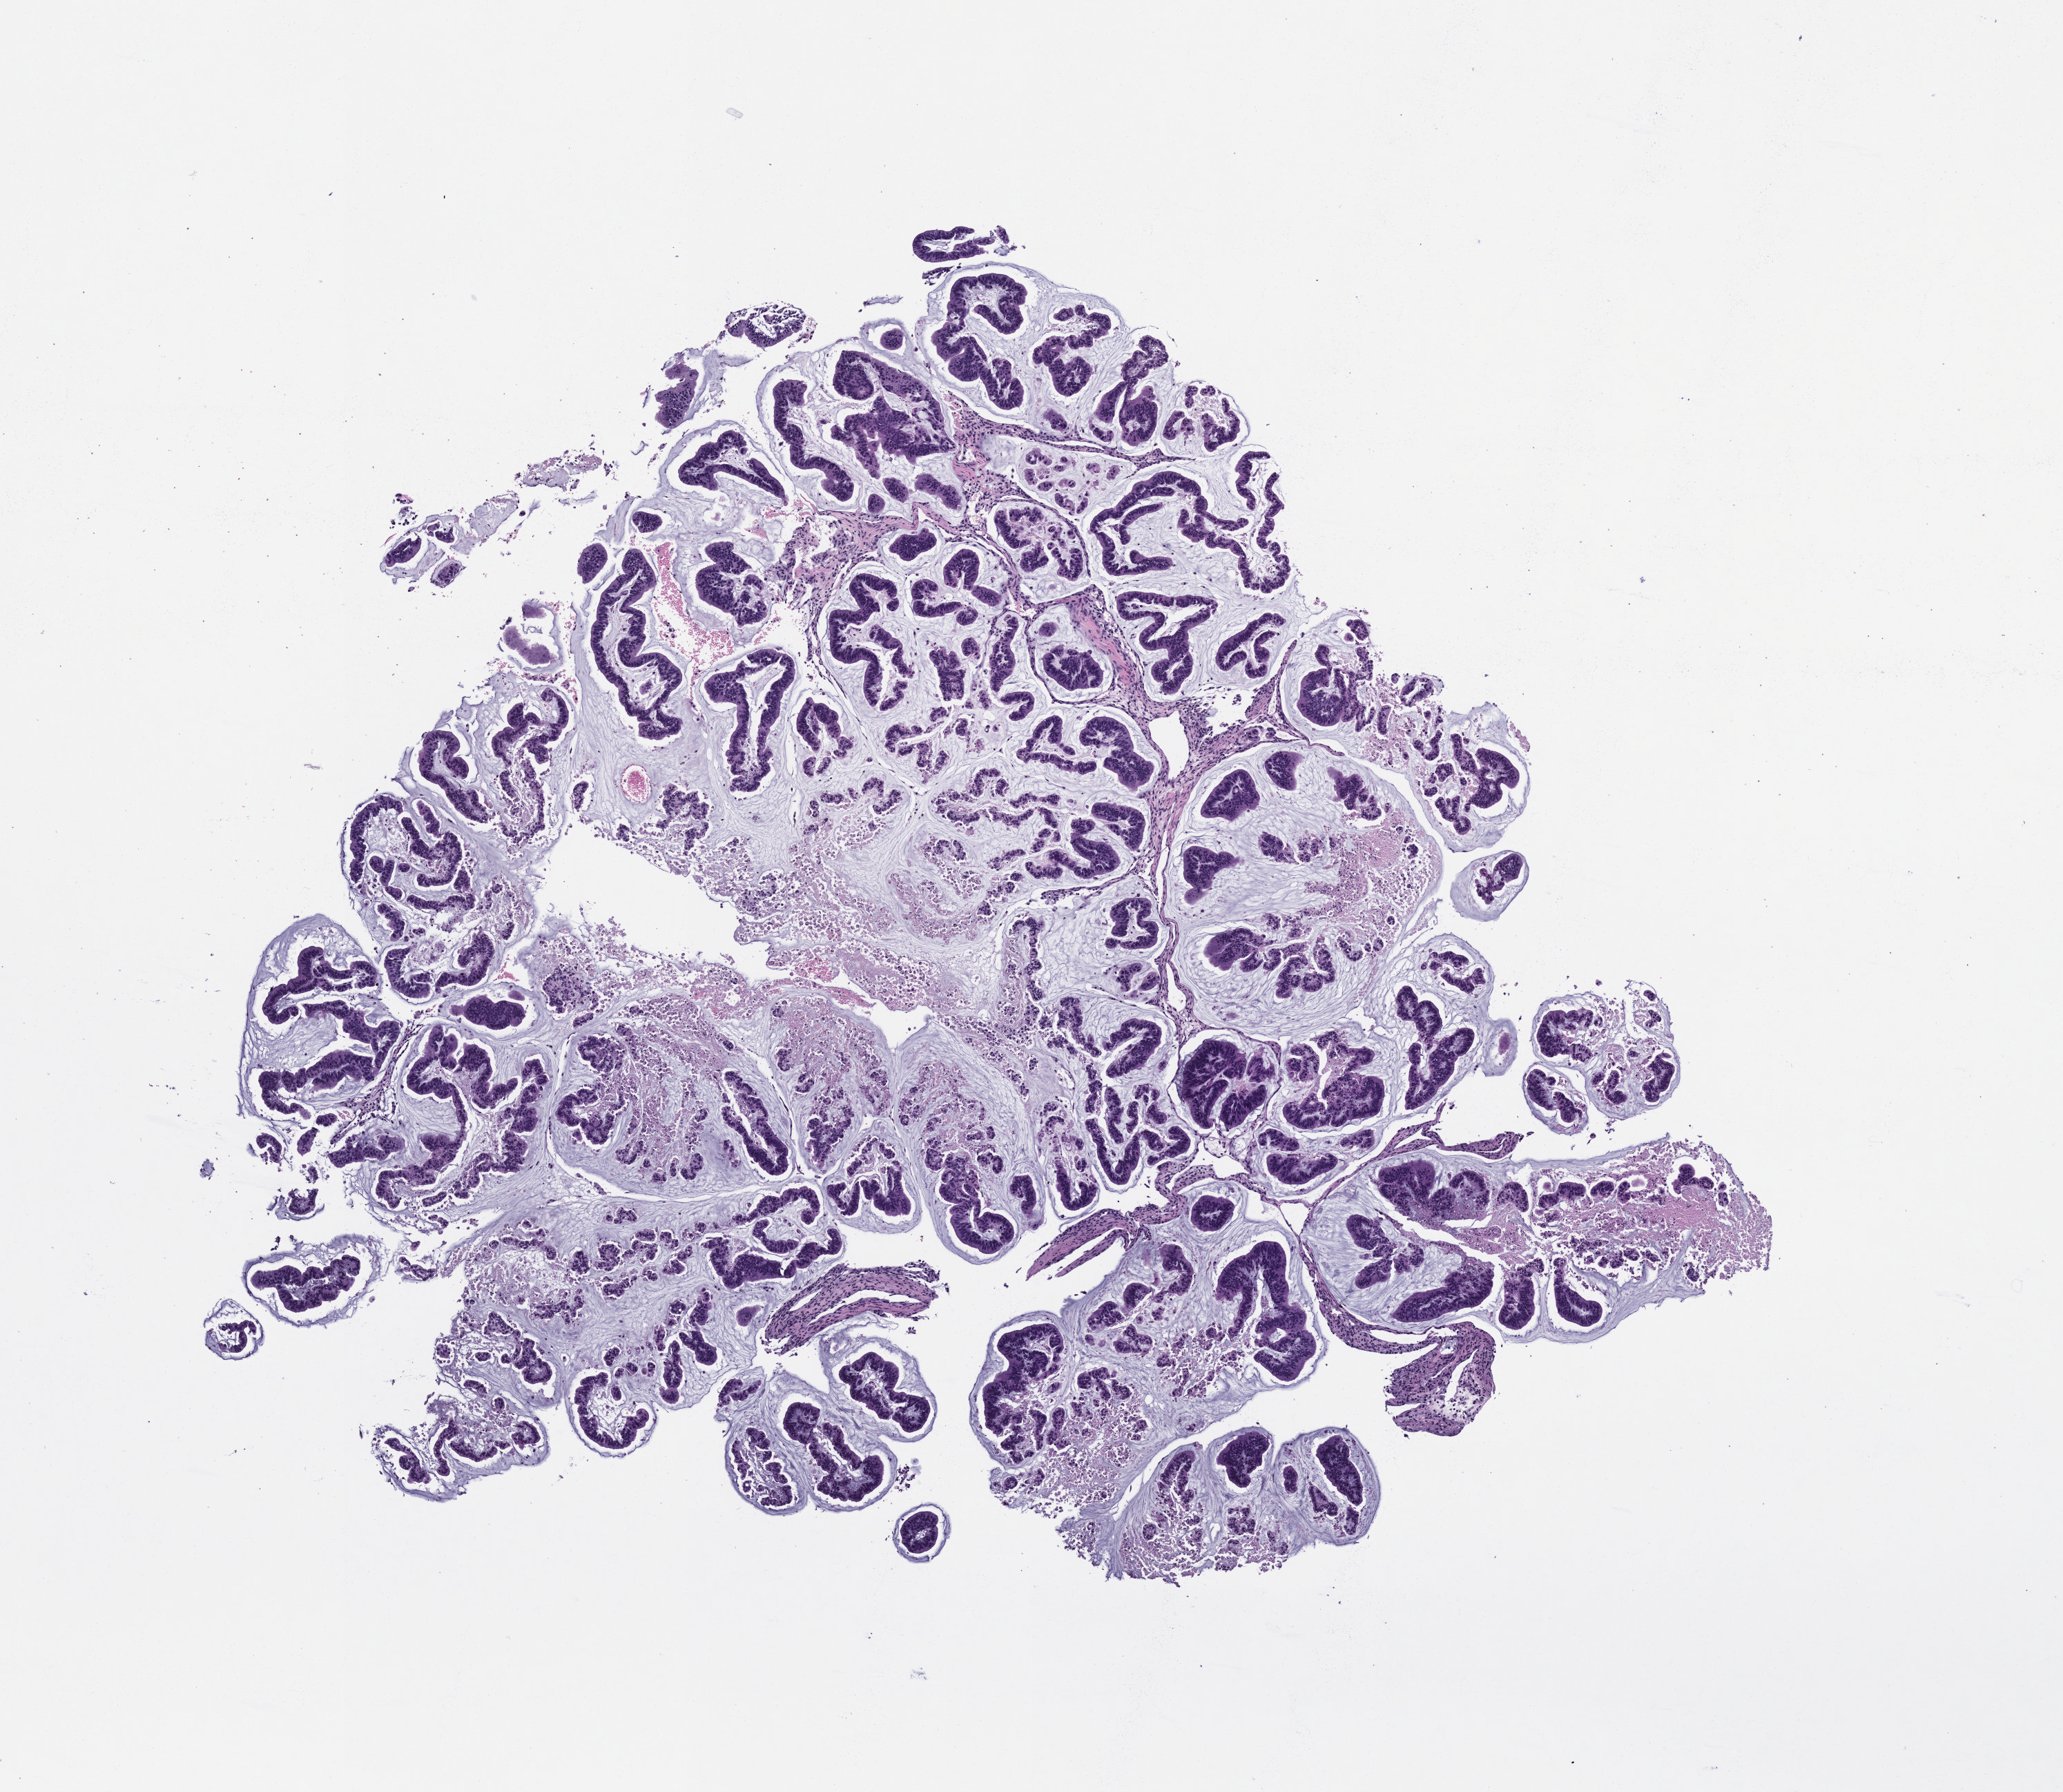
Whole-slide image, hematoxylin and eosin (H&E): patient-derived xenograft (human tumor grown in a mouse), passage 2, low-resolution overview of the scanned area, about 6.0 x 5.2 mm. FFPE section. Originating tumor site category: colon.
Originating patient diagnosis: Colon Adenocarcinoma.